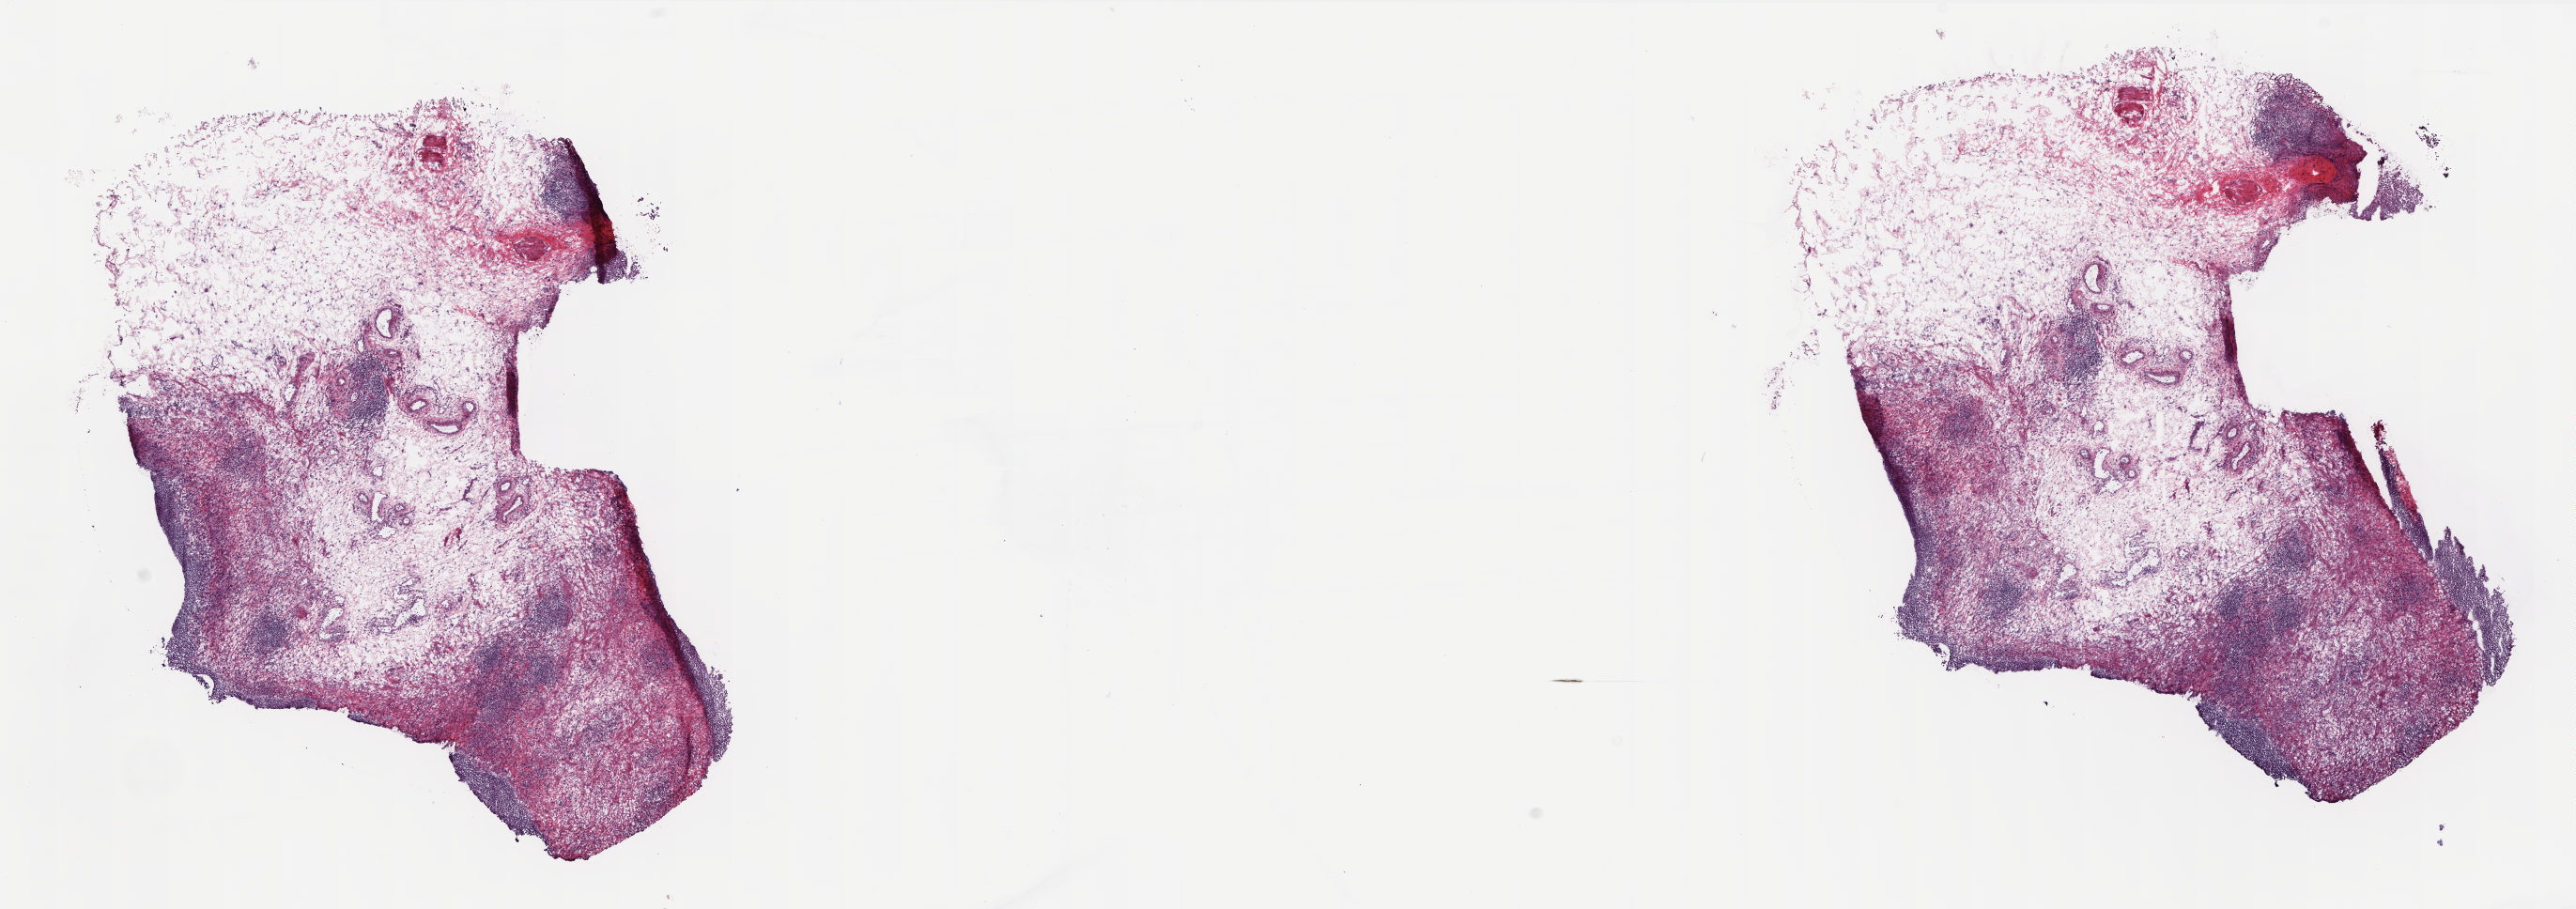
Whole-slide histology image, Hematoxylin and eosin (H&E) stained — shown as a low-resolution overview of the whole scanned area (about 22.1 x 7.8 mm, slide scanned at 20x); frozen section; solid tissue normal (non-tumour tissue) sample from the bladder. Patient: female, age at initial diagnosis 67 years. Pathologist review of this section (percent, as recorded): tumour cells 0%, tumour nuclei 0%, normal cells 8%, stromal cells 92%, necrosis 0%. Inflammatory infiltration, as recorded: lymphocyte infiltration 20%, monocyte infiltration 2%, neutrophil infiltration 3%.
- this section: solid tissue normal (non-tumour) sample from the same patient
- patient diagnosis: Transitional cell carcinoma (posterior wall of bladder)